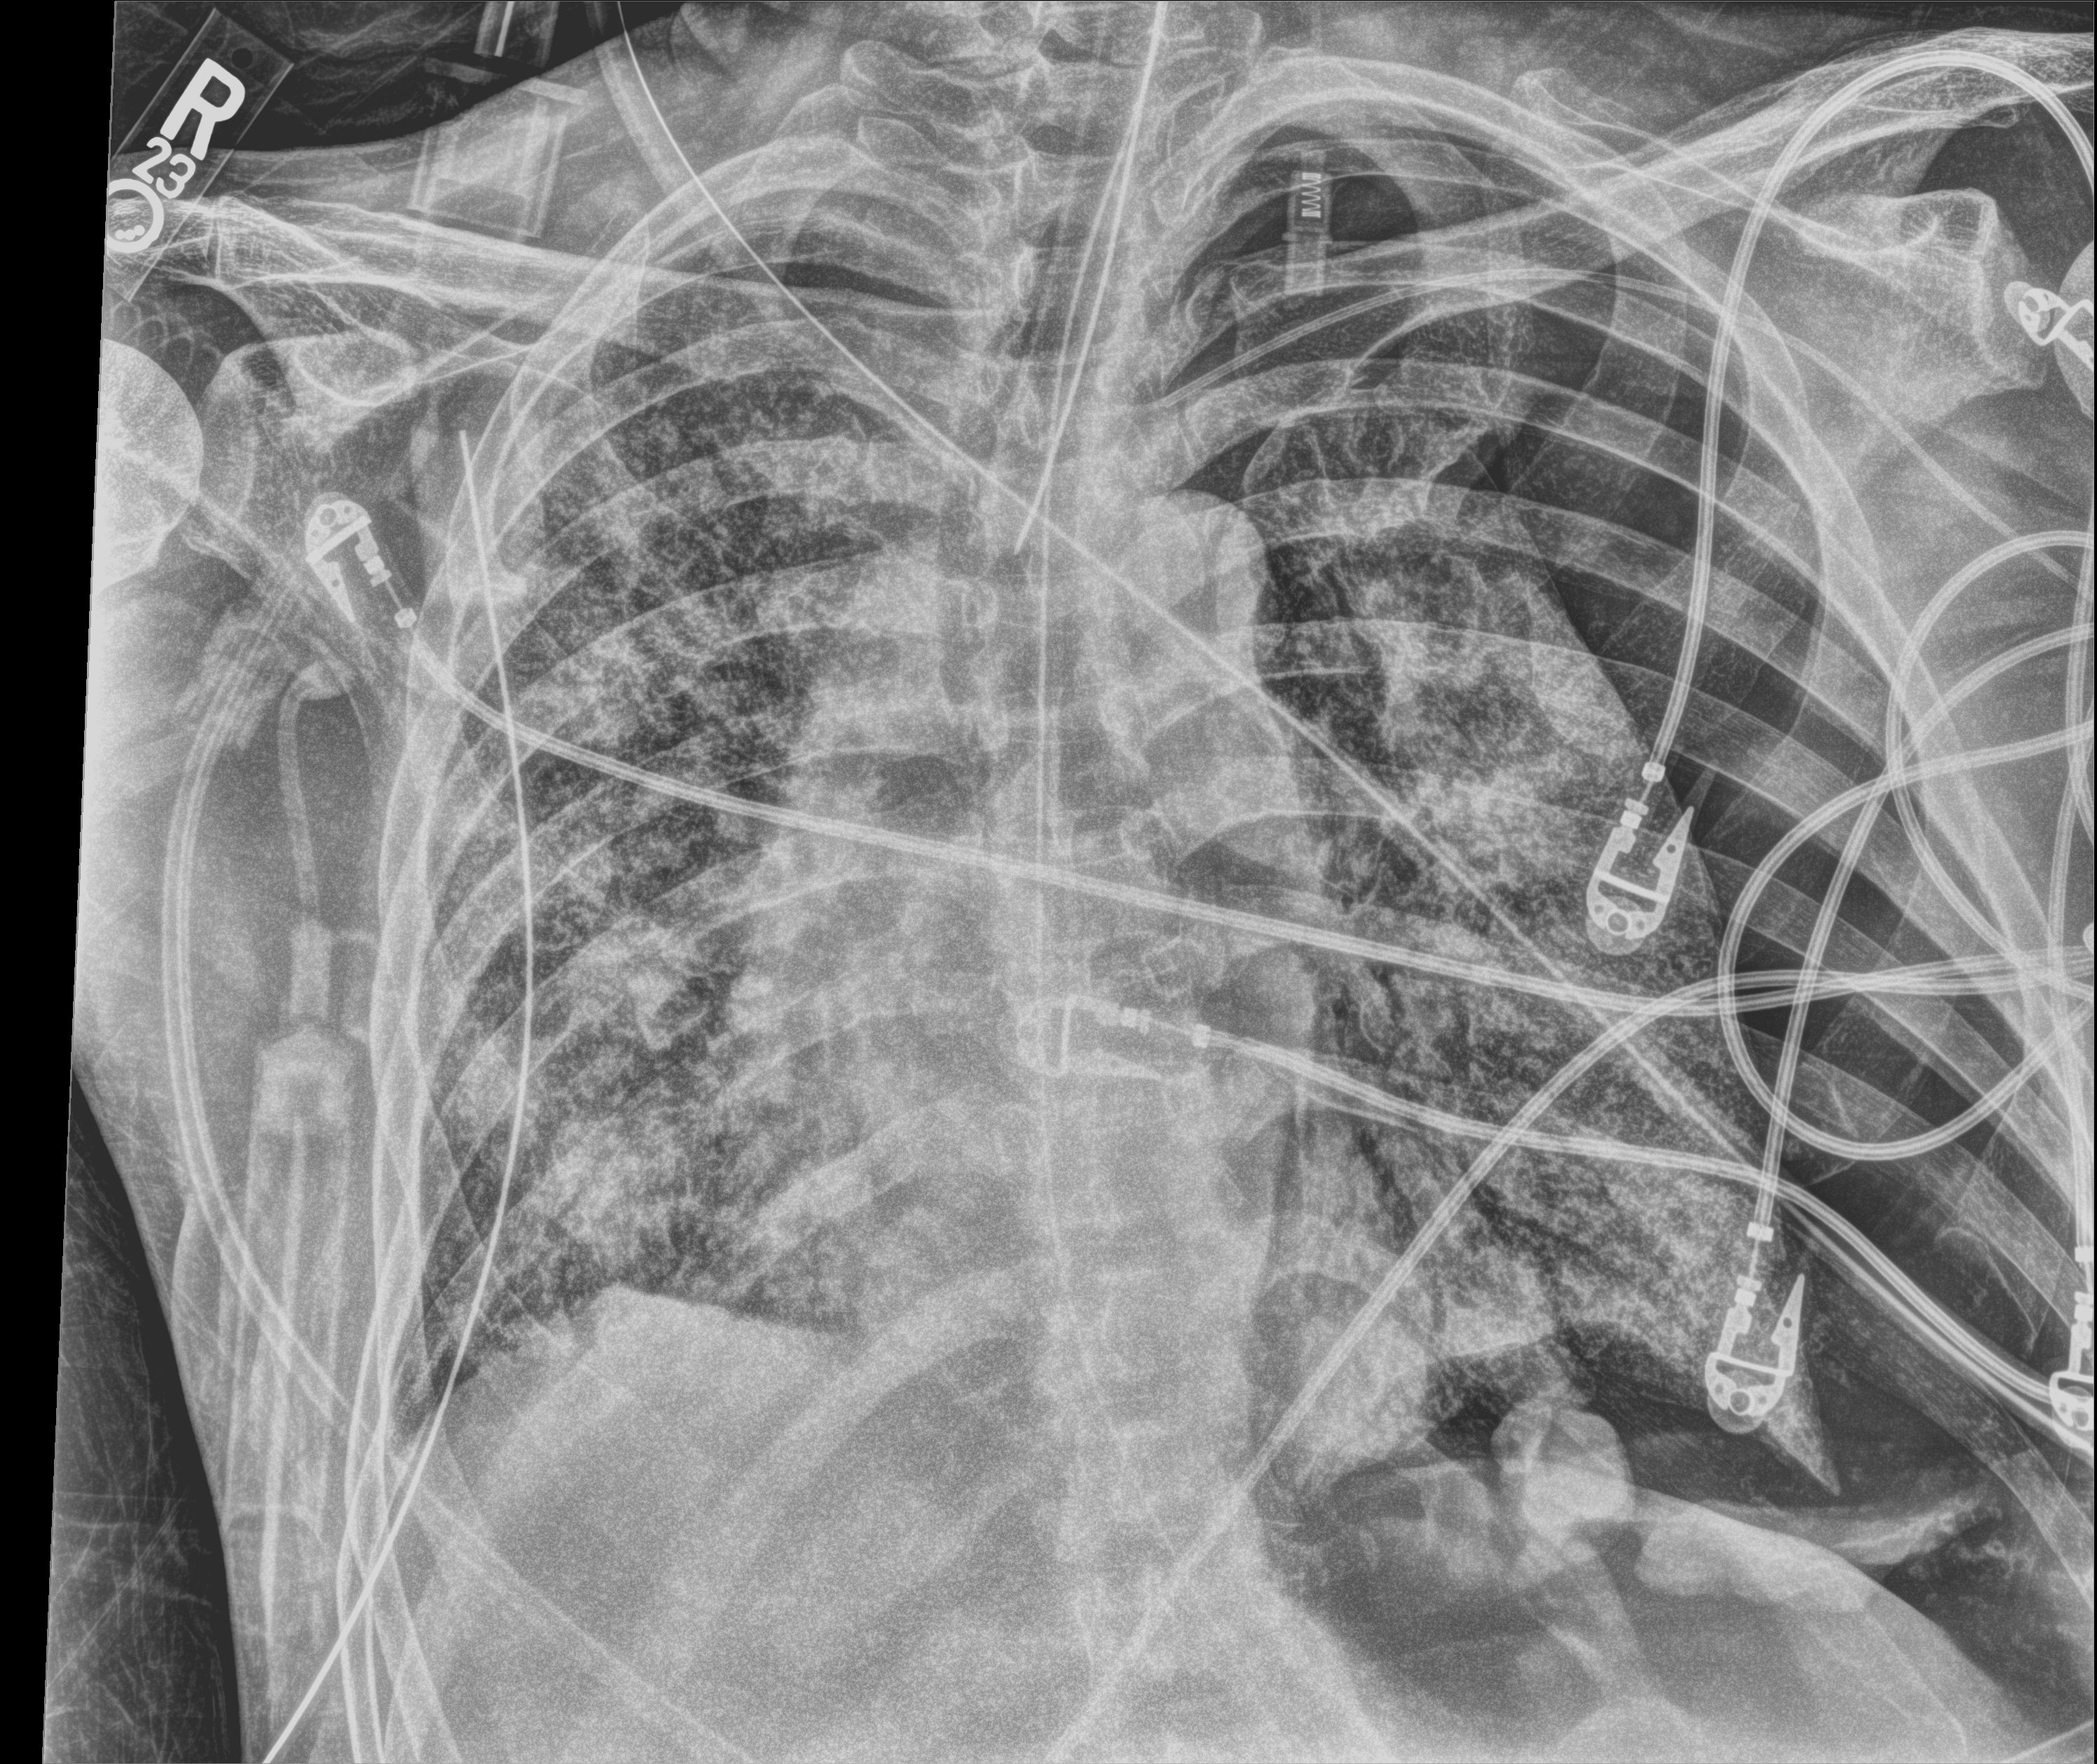
Chest X-ray (portable), anteroposterior (AP) projection. Male patient hospitalised with COVID-19, age 60–74 years.
Hospital-stay facts (about this admission, not read from this image; timing relative to this image not recorded): admitted to intensive care during this hospital stay: yes.